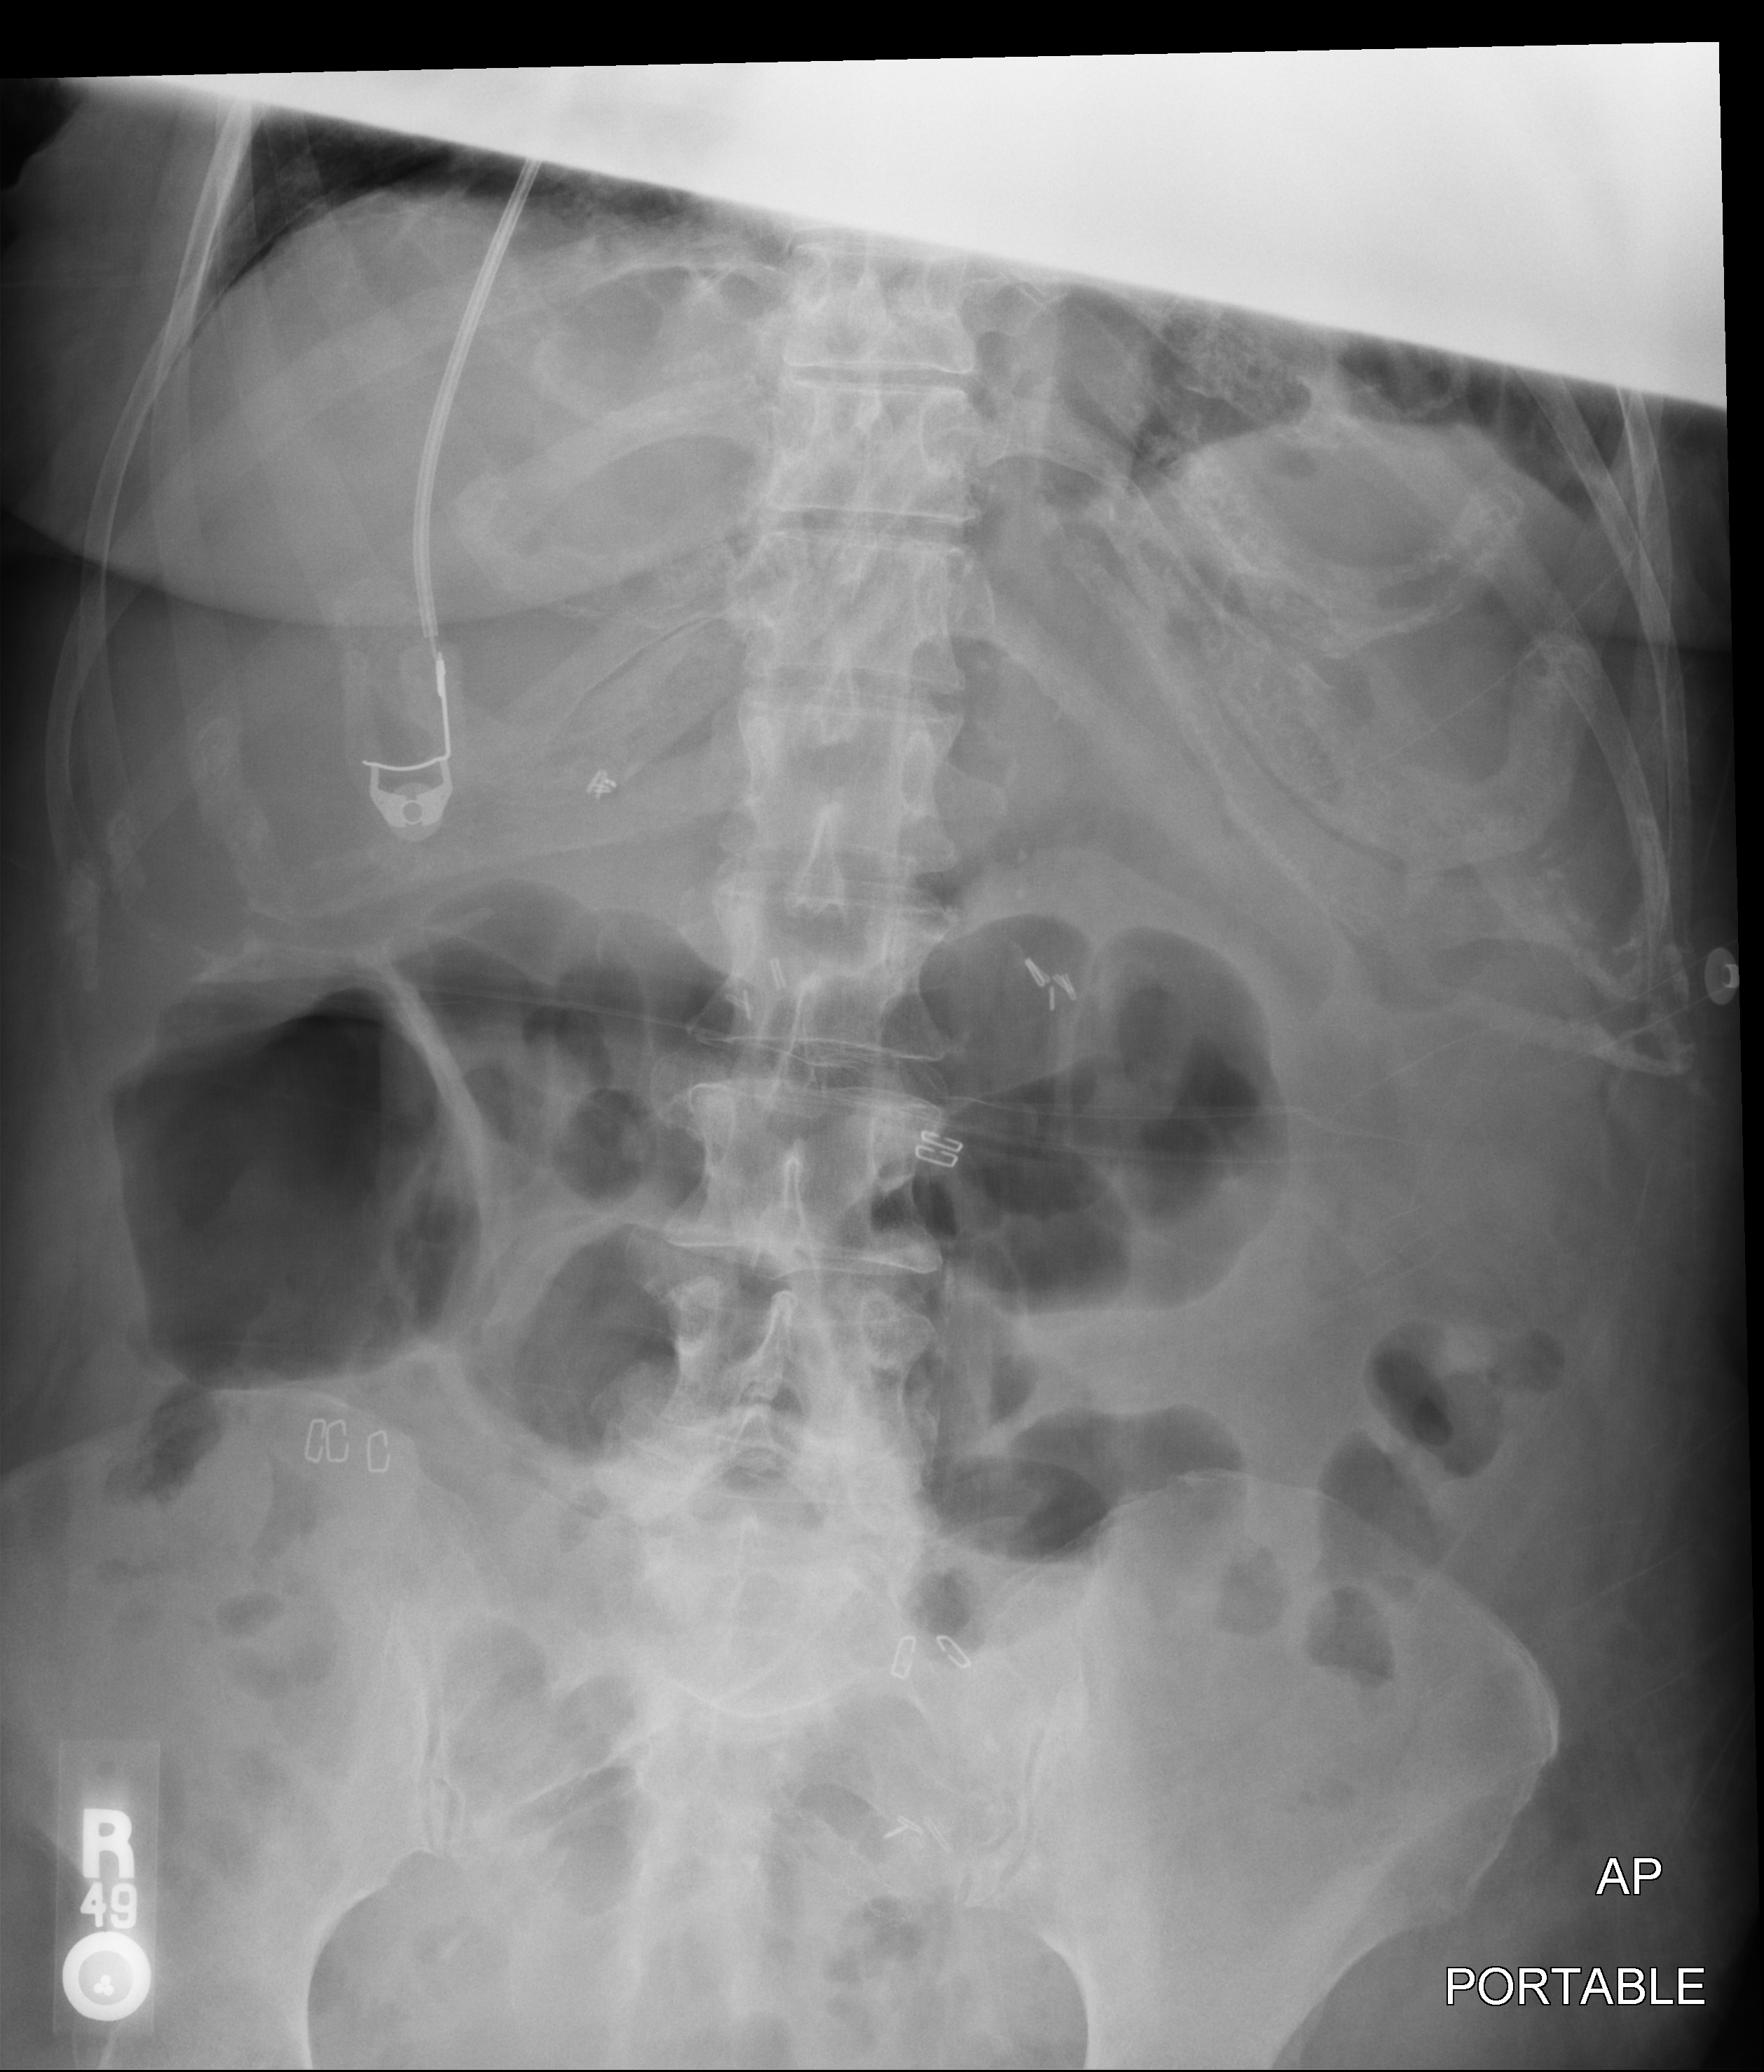
Portable abdomen radiograph, anteroposterior (AP) projection. Patient hospitalised with COVID-19; female, aged 18–59 years.
Hospital-stay facts (about this admission, not read from this image; timing relative to this image not recorded):
- admitted to intensive care during this hospital stay: no